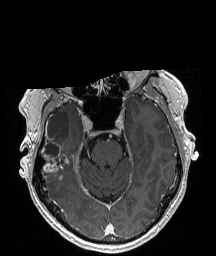
Brain MRI from a brain-tumour surgery series, one axial slice. Slice 133 of 208 in the series (ordered by position). T1-weighted post-contrast. 216 × 256 image matrix, field of view 211 × 250 mm. From the clinical record (not read from this slice): histopathology: Astrocytoma; WHO grade: 4; IDH mutation: yes; tumour location: Right Temporal.
Annotated regions visible in this slice (expert manual segmentation):
- tumour: bounding box <42,142,61,179> (left, top, right, bottom; pixels)